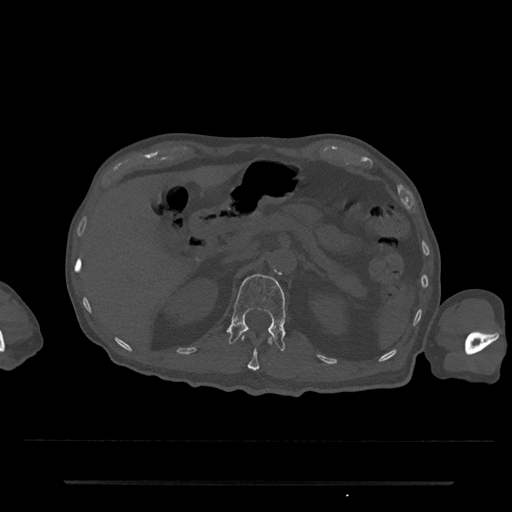
CT including the spine, one axial slice; position 151 of 797 along the scan axis; bone window (W 1800 / L 400 HU); 0.5 mm slice thickness; 512 × 512 image matrix, field of view 427 × 427 mm. Patient: male, 74 years. From the clinical record (not read from this slice): primary cancer: prostate.
Annotated regions visible in this slice (semi-automatically segmented with operator editing):
- L1 vertebra: bounding box <228,274,286,353> (left, top, right, bottom; pixels)
- T12 vertebra: <242,335,273,371>